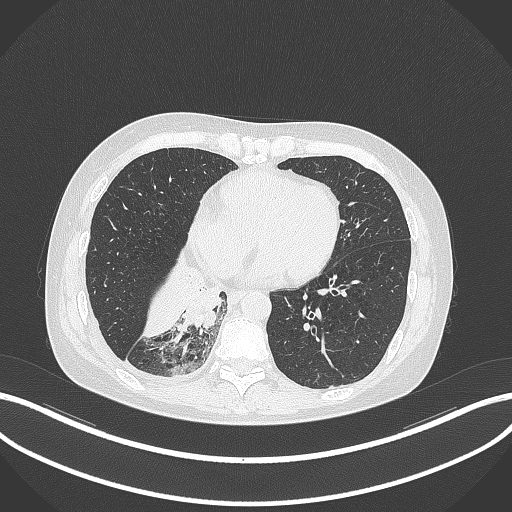
Chest CT, one axial slice. Slice 105 of 329 in the series (ordered by position). Reconstruction kernel B70f. Lung window (W 1500 / L -600 HU). 1 mm slice thickness. 512 × 512 image matrix, field of view 400 × 400 mm. Patient: female, 63 years. Case-level facts recorded for this patient, not image findings: clinical TNM (as recorded): T1c N0 M0.
Structures marked on this image (bounding box drawn by a radiologist):
- lung tumour (recorded histology: adenocarcinoma): box from (x=180, y=283) to (x=229, y=333) px